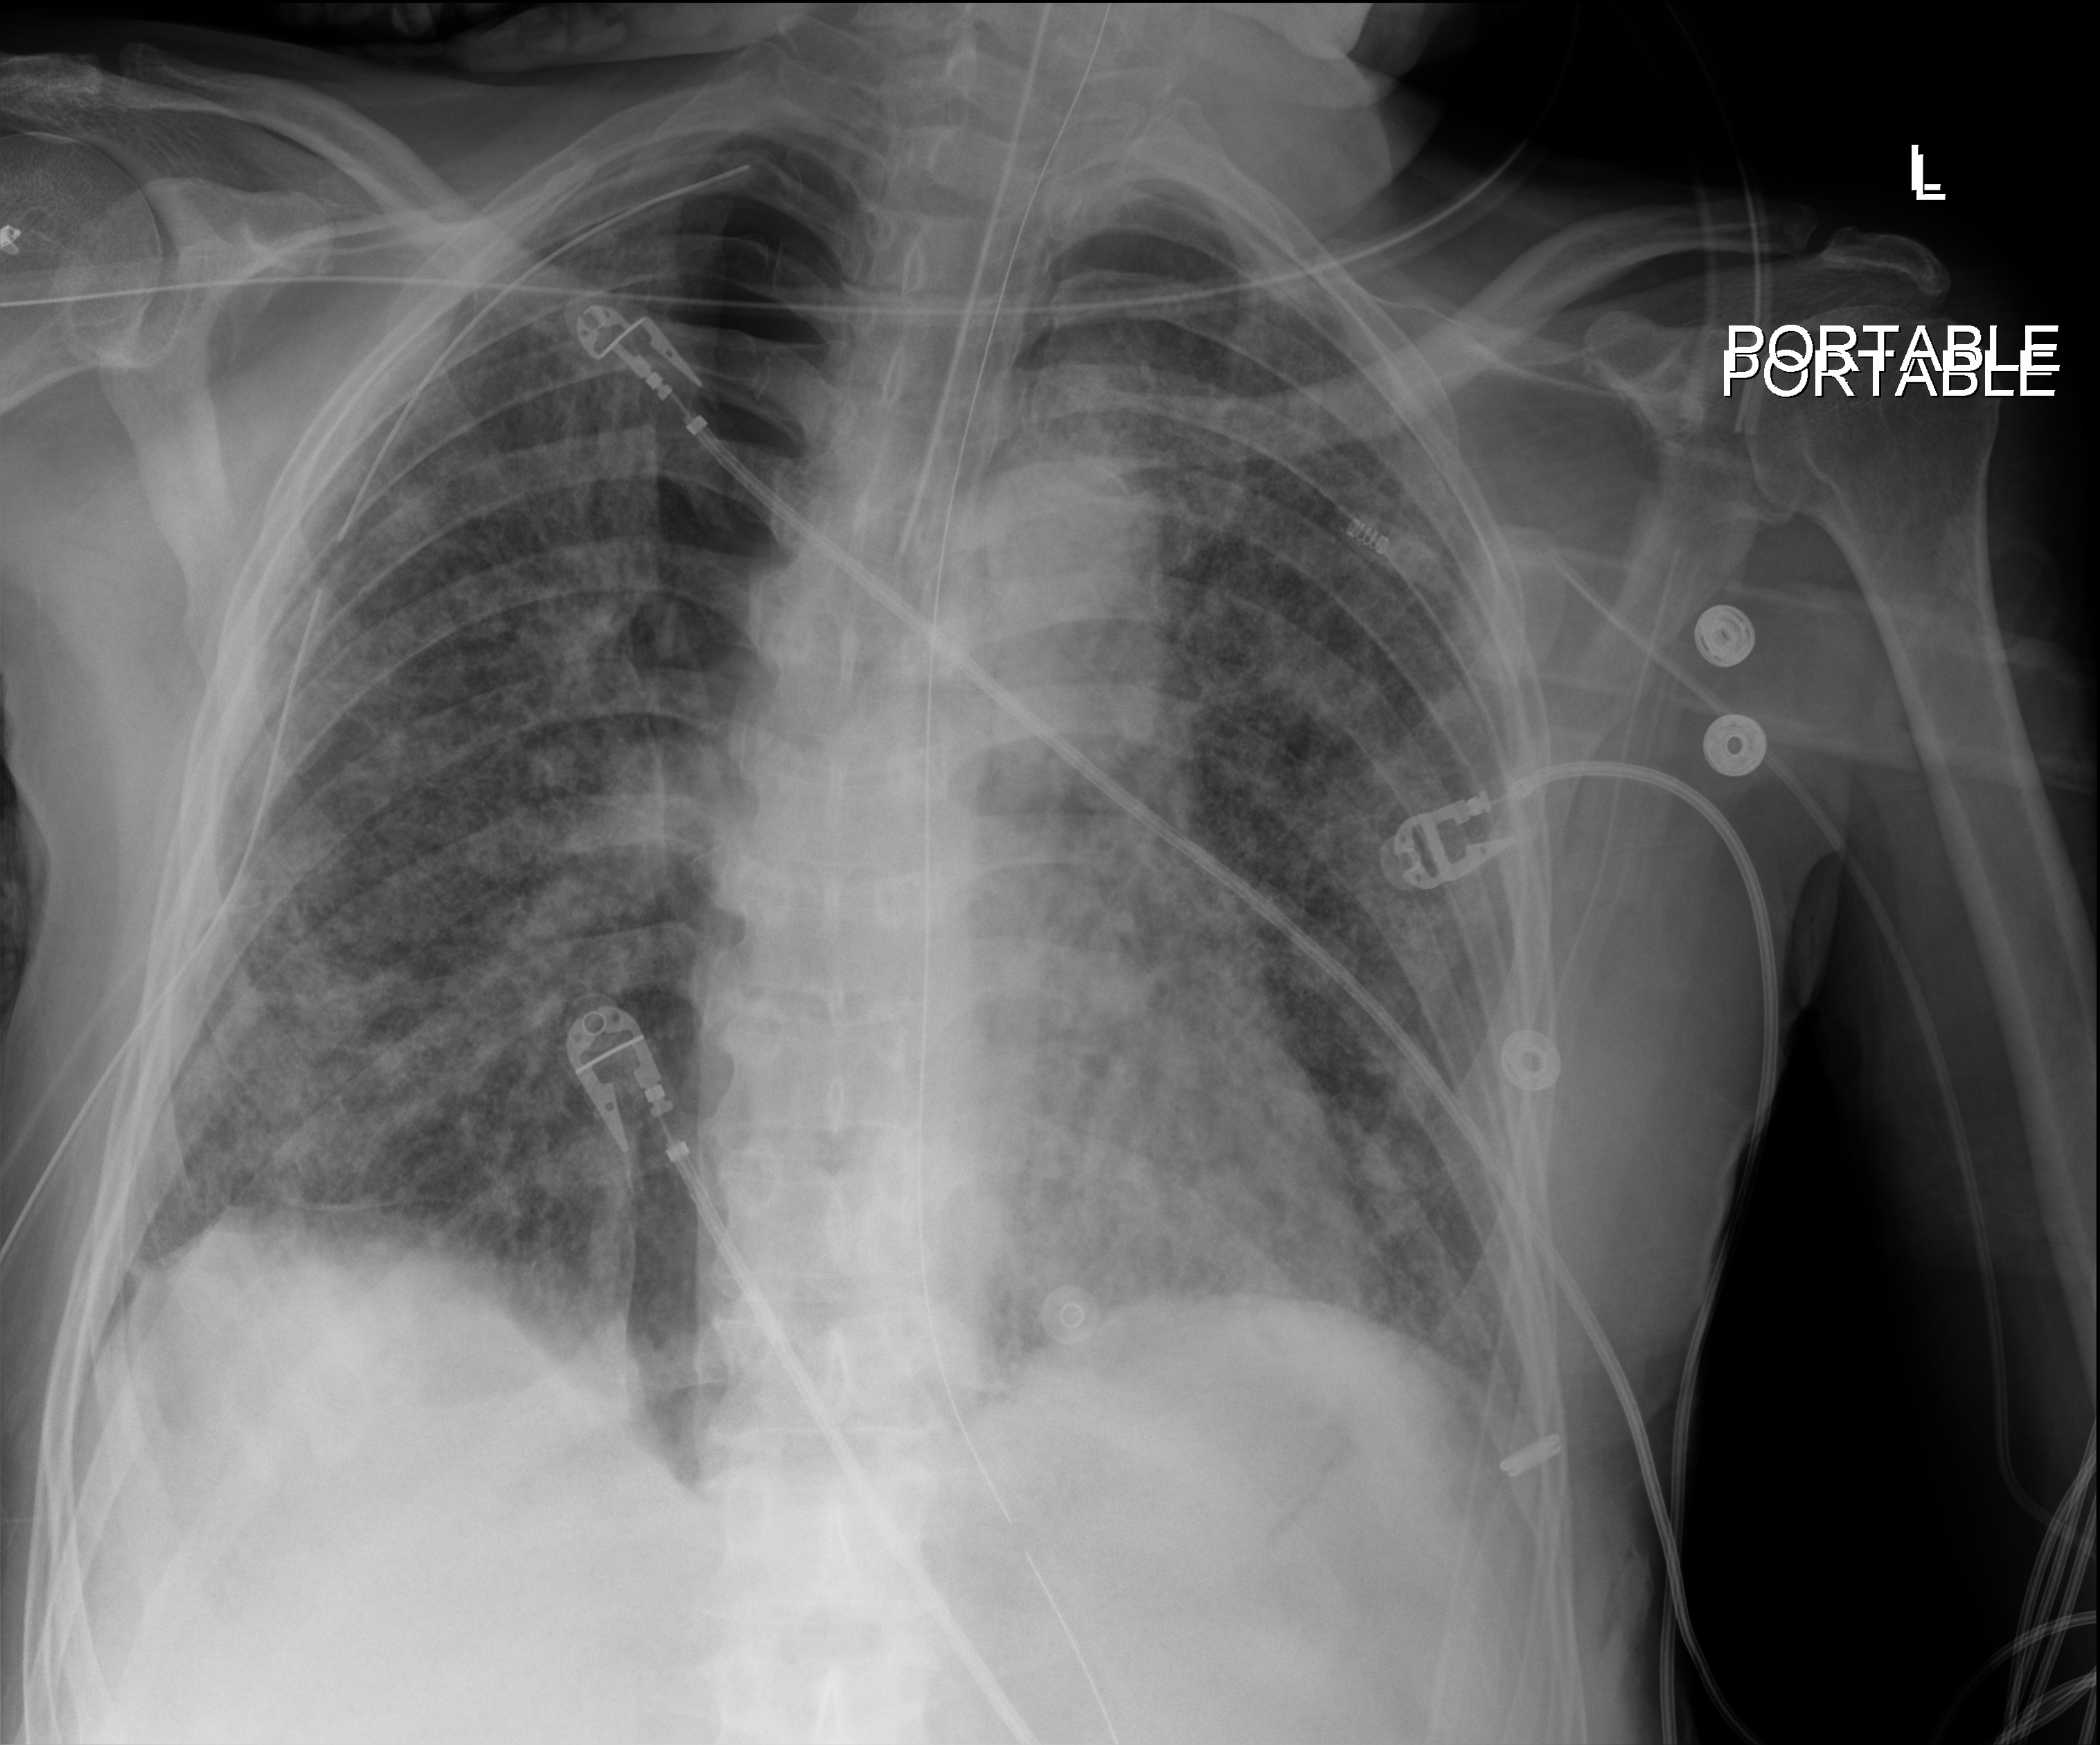
Portable chest radiograph, anteroposterior (AP) projection. Male patient hospitalised with COVID-19, age 60–74 years.
From the hospital-stay record, not from the radiograph (when in the stay this image was taken is not recorded):
- admitted to intensive care during this hospital stay: yes
- length of hospital stay: 65 days